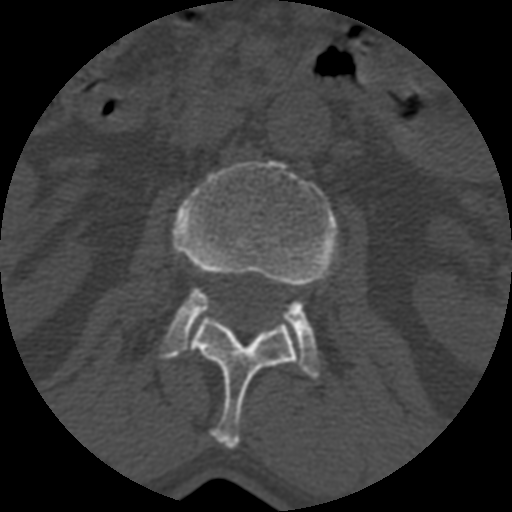
CT including the spine, one axial slice; position 347 of 399 along the scan axis; 120 kVp; bone window (W 1800 / L 400 HU); 512 × 512 image matrix. Patient age 71 years. Case-level facts recorded for this patient, not image findings: primary cancer: prostate.
Outlined on this slice (semi-automatically segmented with operator editing):
- L1 vertebra: box from (x=190, y=316) to (x=296, y=447) px
- L2 vertebra: (x=160, y=160)–(x=339, y=379)